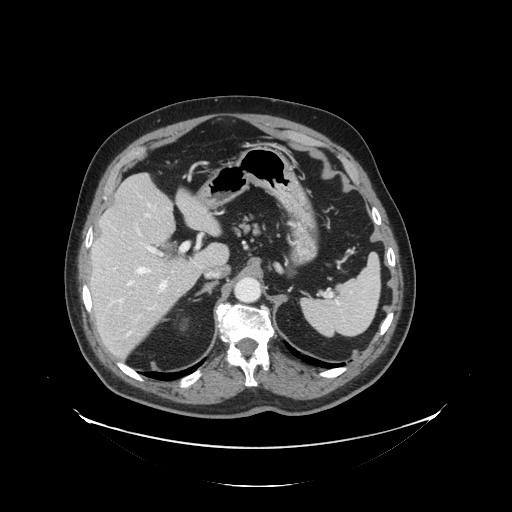
Contrast-enhanced abdominal CT, one axial slice. Slice 90 of 138 in the series (ordered by position). Reconstruction kernel STANDARD. 120 kVp. Intravenous contrast given. Soft-tissue window (W 400 / L 40 HU). 2.5 mm slice thickness. 512 × 512 image matrix, field of view 497 × 497 mm. Male patient, age 77 years. Case-level facts recorded for this patient, not image findings: diagnosis: colorectal cancer liver metastases, imaged before liver resection; multiple liver metastases: no; largest metastasis: 1.5 cm; disease in both lobes: no.
Outlined on this slice (outlined manually by an expert reader):
- hepatic veins: bounding box <126,204,152,336> (left, top, right, bottom; pixels)
- liver: <91,174,228,358>
- planned liver remnant (the part of the liver to remain after resection): <92,174,226,288>
- portal vein (with intrahepatic branches): <116,243,189,304>